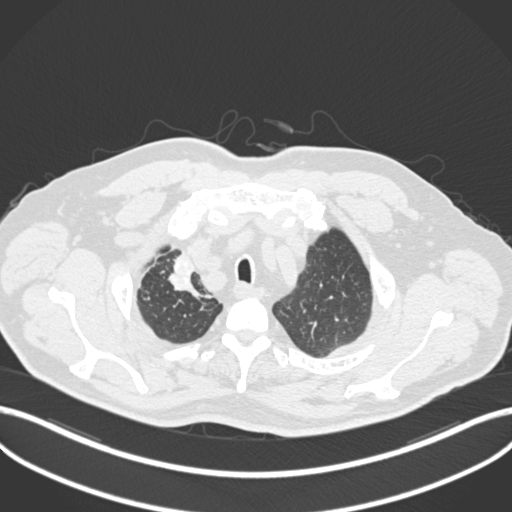
Chest CT, one axial slice; position 176 of 255 along the scan axis; lung window (W 1500 / L -600 HU); 1 mm slice thickness; 512 × 512 image matrix, field of view 400 × 400 mm. Patient: male, 60 years. From the clinical record (not read from this slice): clinical TNM (as recorded): T1b N1 M0.
Annotated regions visible in this slice (rectangle marked by the reading radiologist):
- lung tumour (recorded histology: squamous cell carcinoma): bounding box <165,253,207,307> (left, top, right, bottom; pixels)